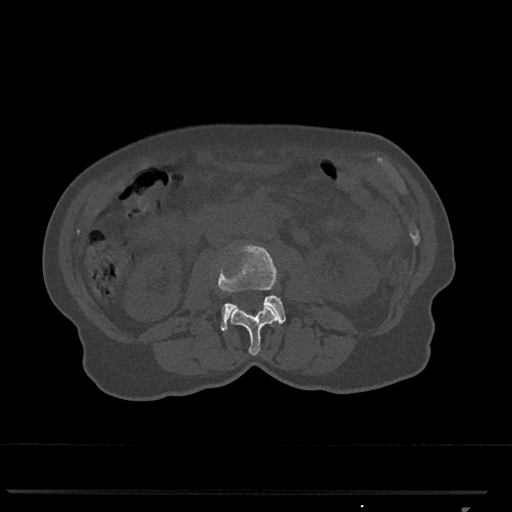
CT including the spine, one axial slice. Position 303 of 793 along the scan axis. Reconstruction kernel Br40s/3. 120 kVp. Bone window (W 1800 / L 400 HU). 0.5 mm slice thickness. 512 × 512 image matrix. Female patient, age 62 years. From the clinical record (not read from this slice): primary cancer: renal.
Structures marked on this image (semi-automatically segmented with operator editing):
- L2 vertebra: bounding box <229,305,278,356> (left, top, right, bottom; pixels)
- L3 vertebra: <218,244,286,331>